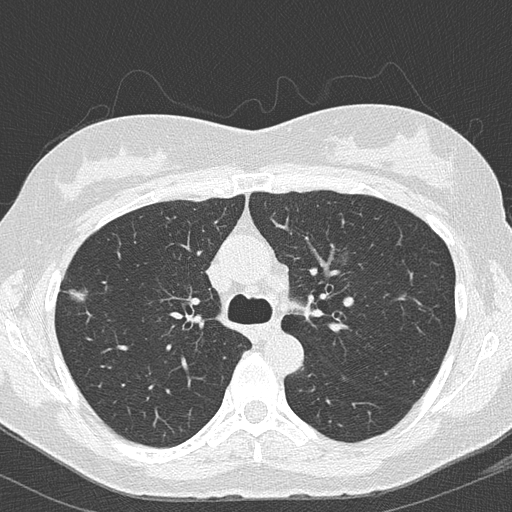
Axial slice from a low-dose chest CT screening exam, second screening round (one year after baseline), lung window (W 1500 / L -600 HU), 2 mm slice thickness, lung (sharp) reconstruction kernel (B50f), slice 47 of 157 in the series, 512 × 512 image matrix, field of view 290 × 290 mm. Female, age 64 years at enrolment. Former smoker at enrolment.
- Lesion marked by an expert reader, bounding box <47,270,102,321> (left, top, right, bottom; pixels).
- The exam's reader record, not a measurement of the box and not confirmed to be the same lesion: non-calcified nodule or mass ≥4 mm, right upper lobe, 16 × 13 mm, mixed attenuation, pre-existing on the prior screen: yes; interval growth: yes.
- Participant outcome: lung cancer diagnosed 112 days after this screen — bronchiolo-alveolar adenocarcinoma, NOS, right upper lobe, well differentiated (G1), stage IA (AJCC 6th edition), 10 mm at pathology.